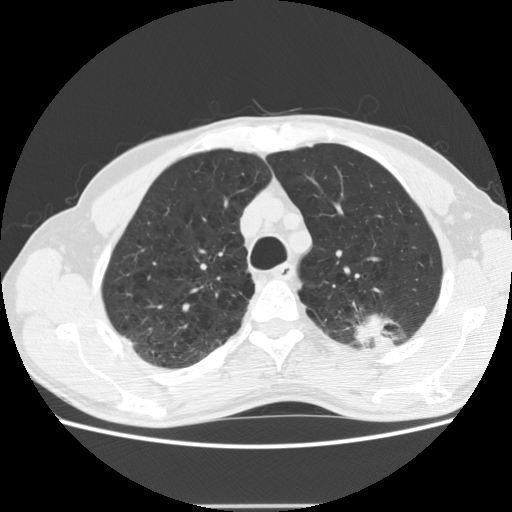
Low-dose screening chest CT, one axial slice. Position 151 of 191 along the scan axis. Reconstruction kernel STANDARD. Lung window (W 1500 / L -600 HU). 512 × 512 image matrix, field of view 352 × 352 mm.
Annotated regions visible in this slice (expert manual segmentation):
- lesion 1 (tumor, upper lobe of left lung): bounding box <355,314,396,349> (left, top, right, bottom; pixels)